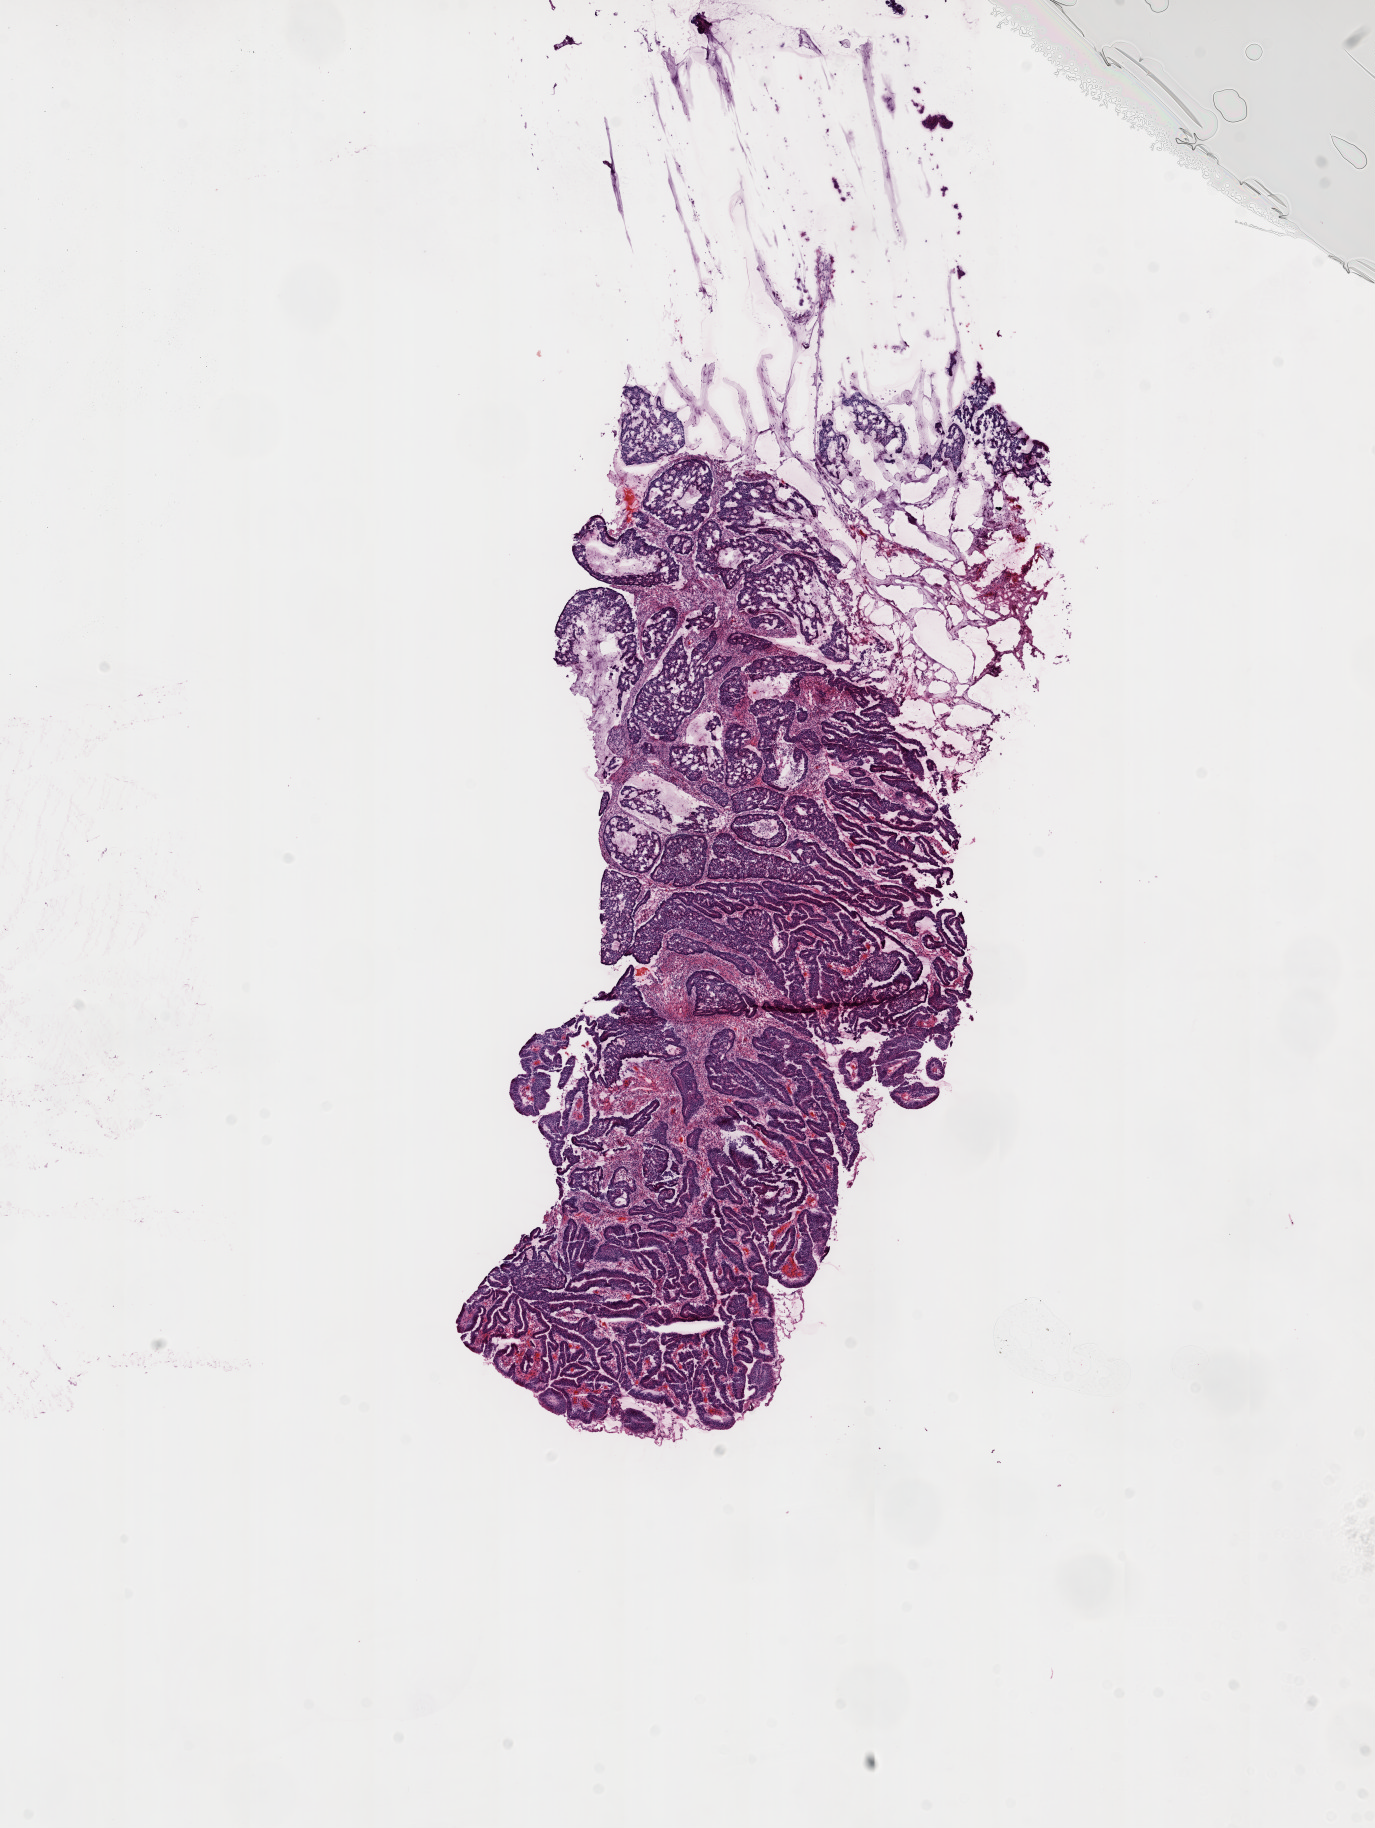
Whole-slide histology image, H&E-stained — low-resolution overview of the scanned area, about 11.0 x 14.7 mm, frozen section, colon, primary tumour sample. Patient: female, age at initial diagnosis 48 years. Pathologist review of this section (percent, as recorded): tumour cells 60%, tumour nuclei 65%, normal cells 20%, stromal cells 10%, necrosis 10%.
- lymph nodes positive (case pathology): 5 of 31 examined
- pathologic diagnosis: Mucinous adenocarcinoma
- AJCC pathologic stage: IIIC (6th edition)